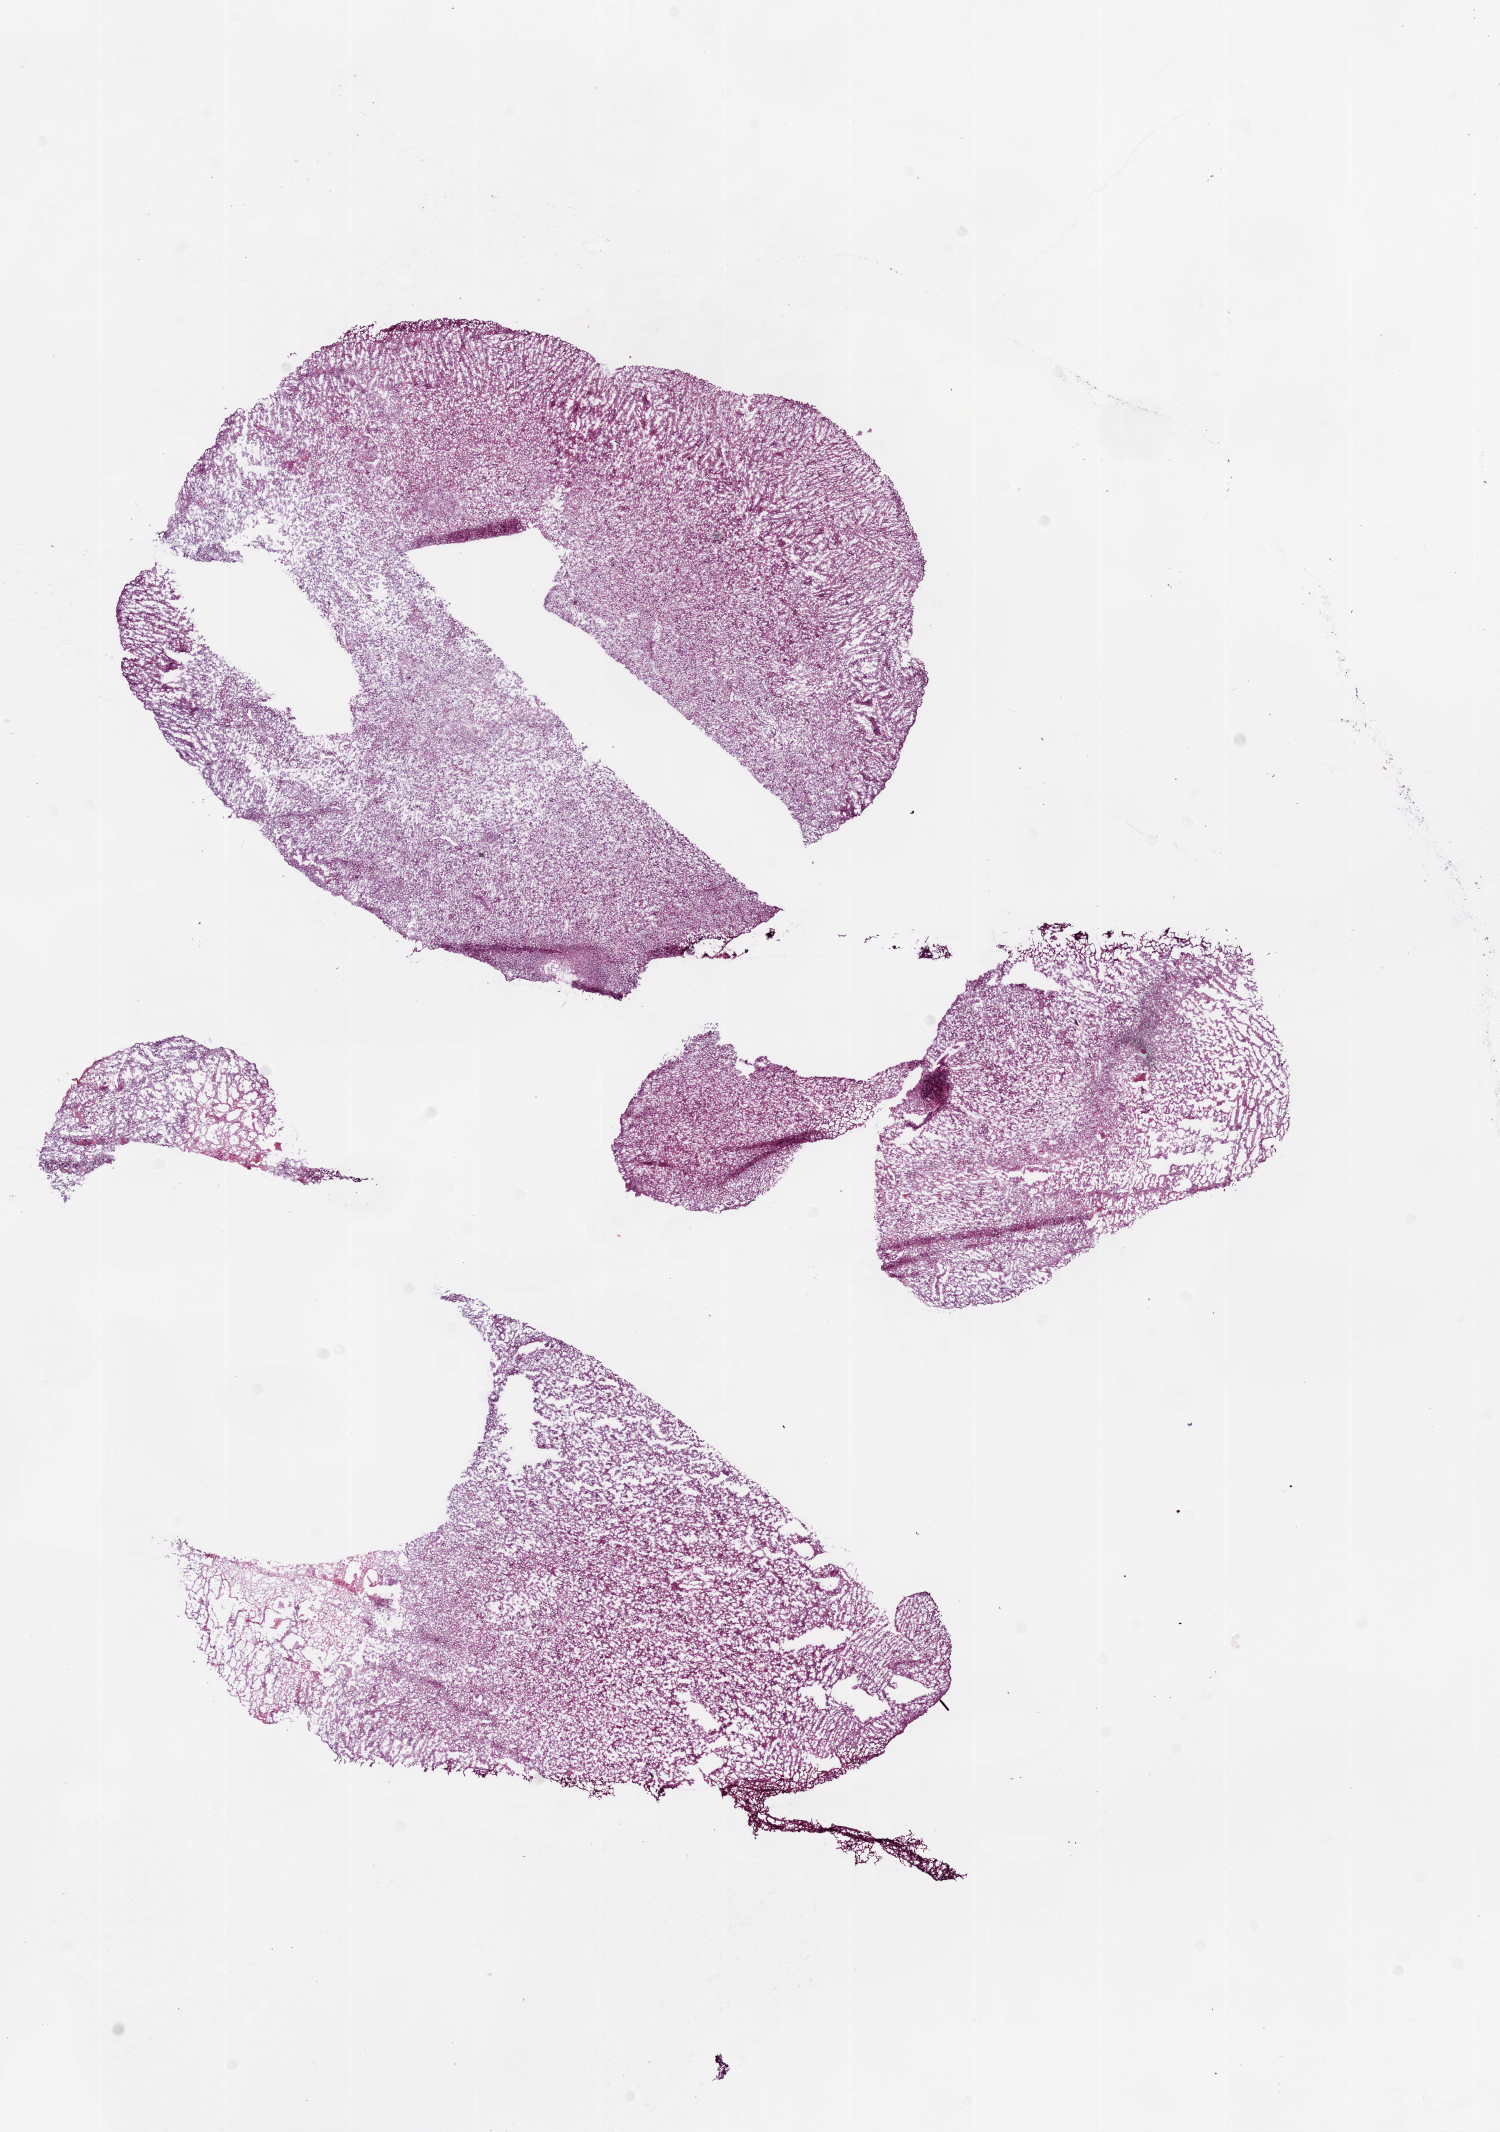
Whole-slide histology image, Hematoxylin and eosin (H&E) stained, low-resolution overview of the scanned area, about 12.0 x 17.1 mm (from a 20x scan), frozen section from the bottom of the tissue portion, brain, primary tumour sample. Female, age 58 years at initial diagnosis. Pathologist review of this section (percent, as recorded): tumour cells 88%, tumour nuclei 95%, normal cells 0%, stromal cells 2%, necrosis 10%.
* pathologic diagnosis: Glioblastoma